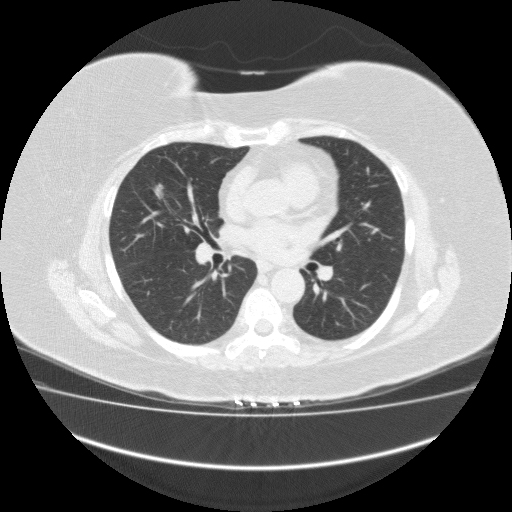
Low-dose screening chest CT, one axial slice. Position 89 of 162 along the scan axis. 120 kVp. Lung window (W 1500 / L -600 HU). 2 mm slice thickness. 512 × 512 image matrix, field of view 420 × 420 mm.
Outlined on this slice (expert manual segmentation):
- lesion 1 (tumor, middle lobe of right lung): bounding box (x1, y1, x2, y2) in pixels: (154, 184, 163, 199)